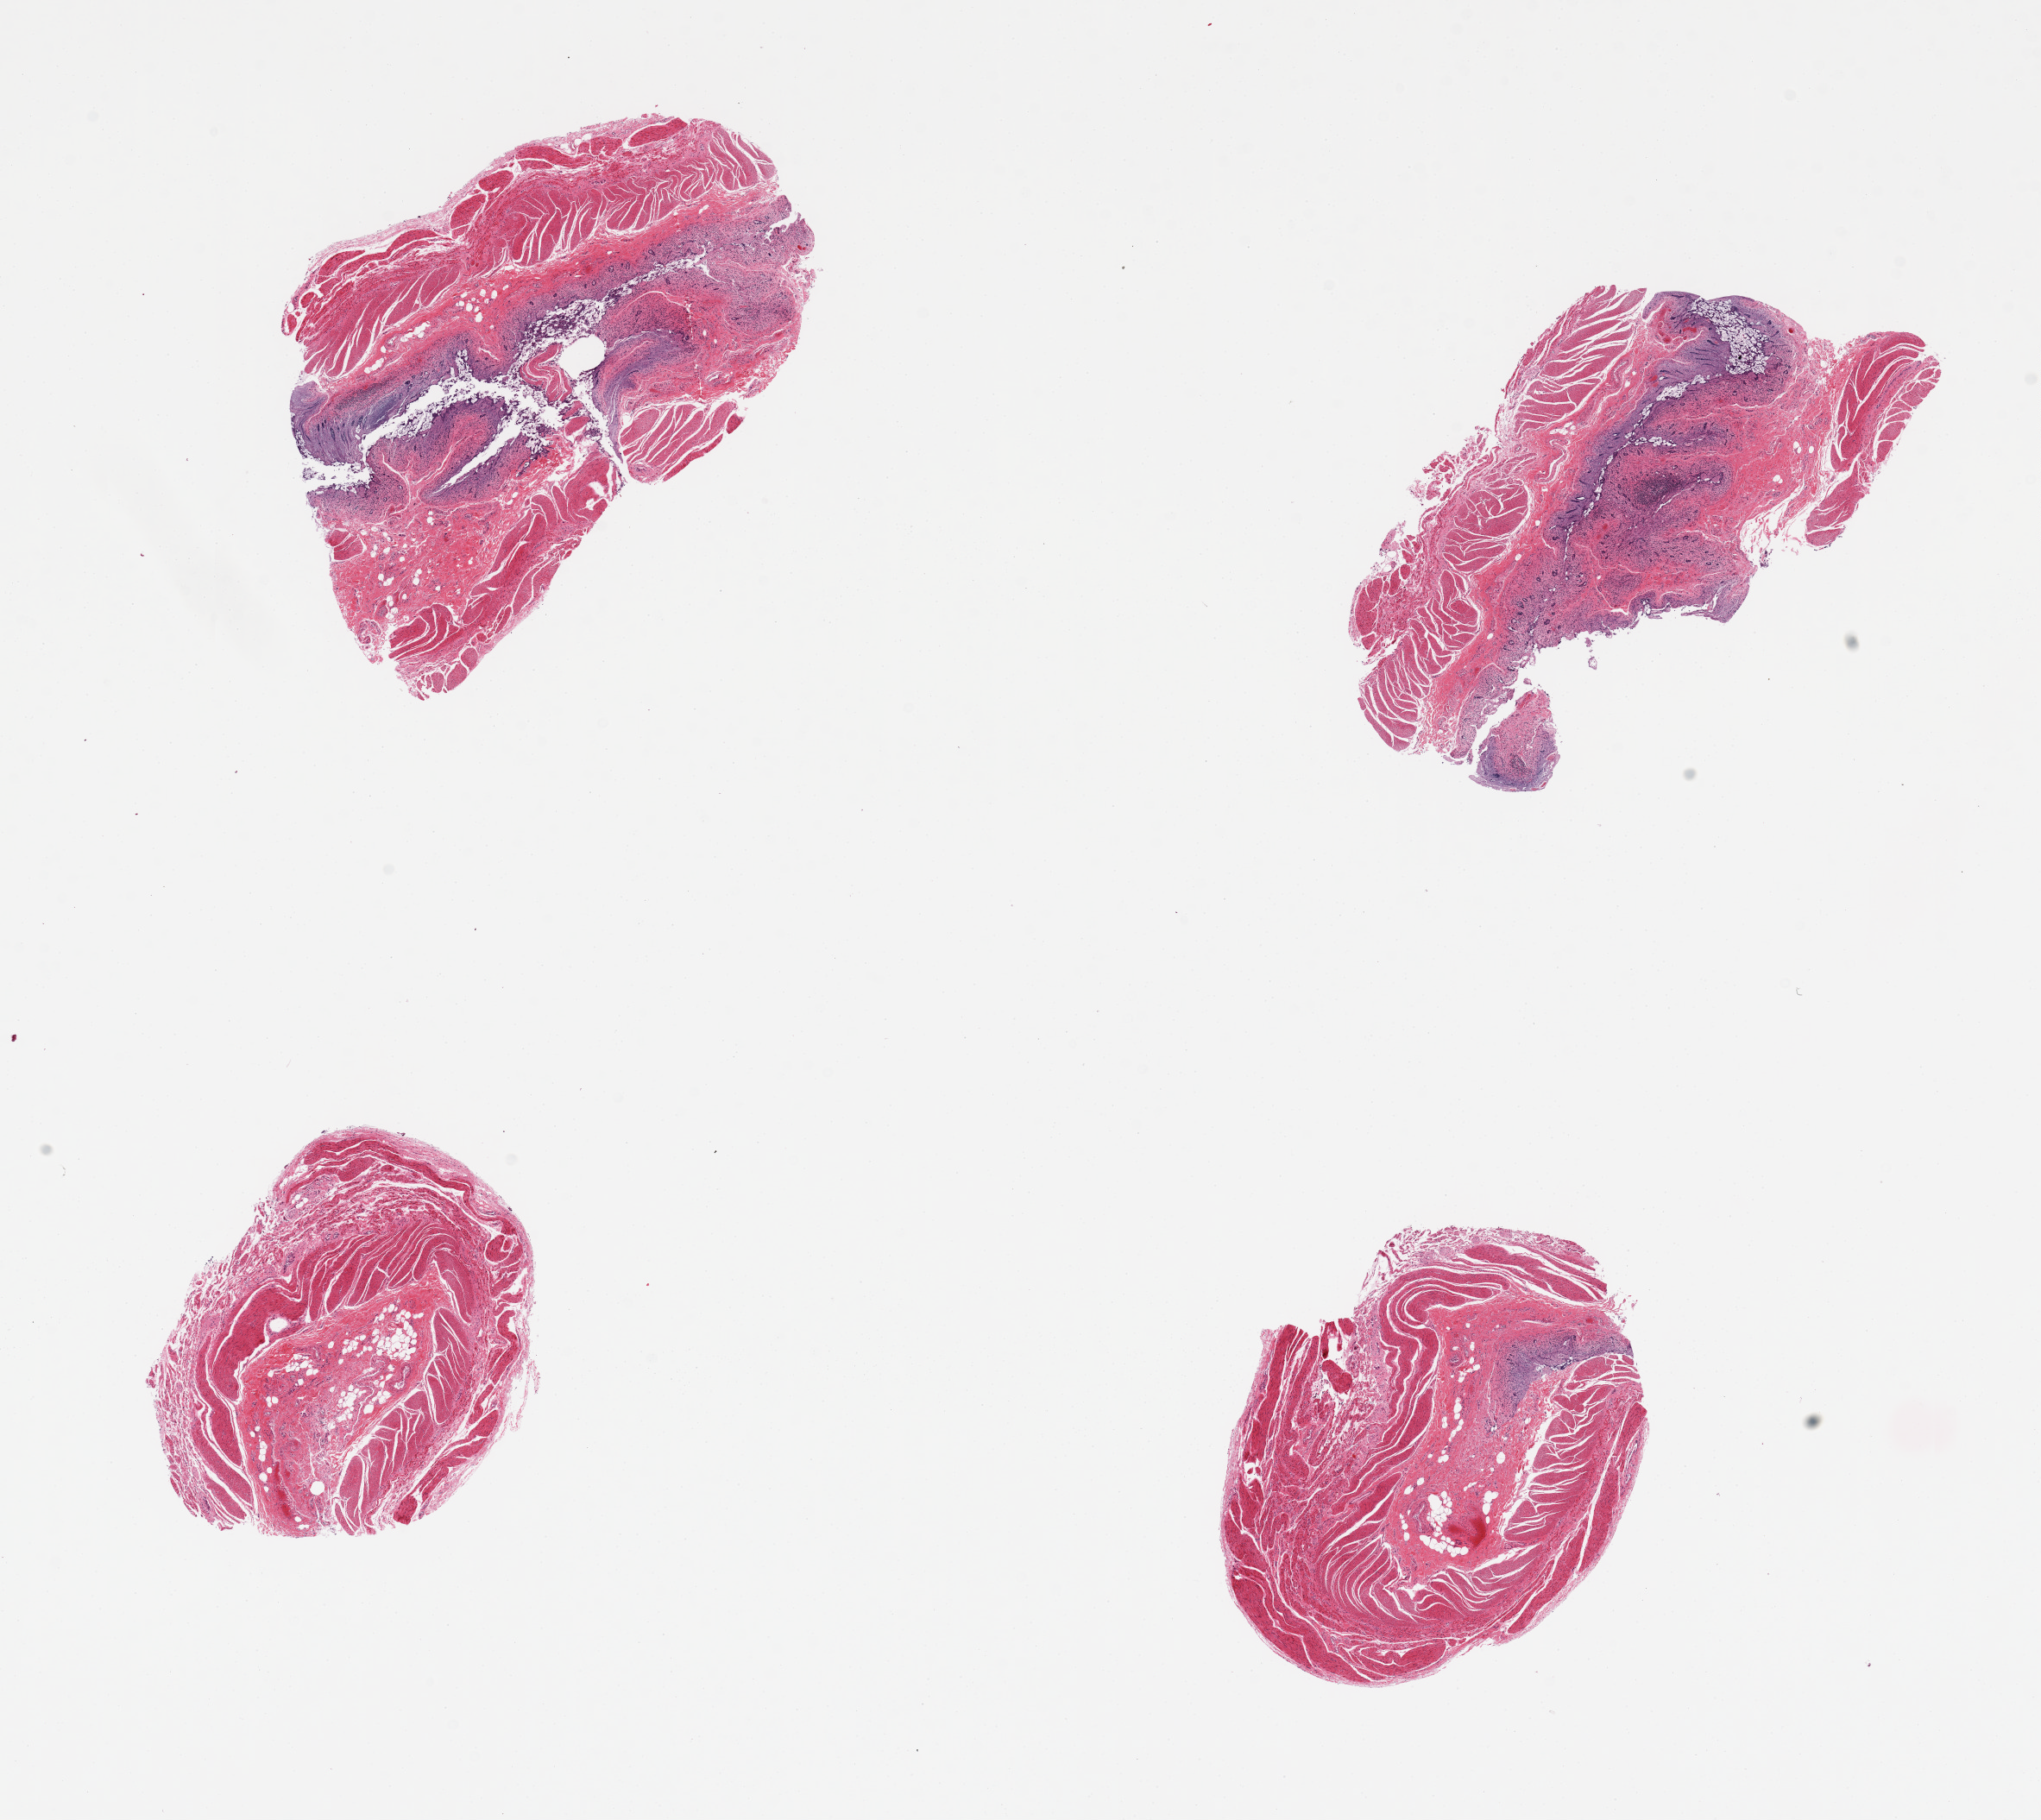
H&E whole-slide image, brightfield — a low-resolution overview of the entire scanned area, about 18.7 x 16.7 mm, PAXgene-fixed, paraffin-embedded tissue, section of ileum (target tissue), tissue donor sample. Donor: male.
Review note (as recorded): 4 pieces, severley autolyzed mucosa and muscularis (not target).